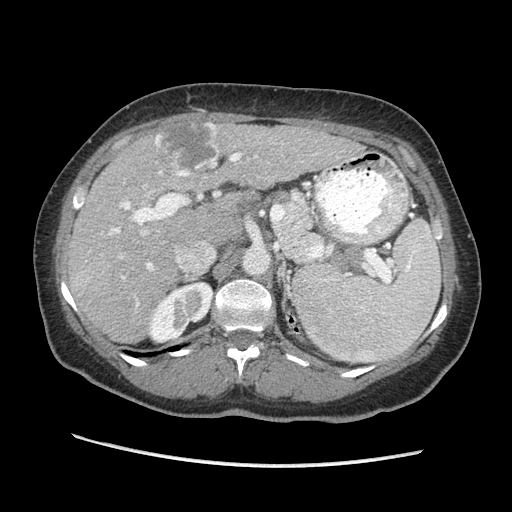
Contrast-enhanced abdominal CT (liver protocol), one axial slice. Slice 132 of 170 in the series (ordered by position). Reconstruction kernel STANDARD. 140 kVp. Soft-tissue window (W 400 / L 40 HU). 512 × 512 image matrix, field of view 360 × 360 mm. From the clinical record (not read from this slice): diagnosis: hepatocellular carcinoma (patient treated with transarterial chemoembolisation; whether this scan precedes or follows treatment is not stated here); TNM stage (as recorded): Stage-II; Child-Pugh class: A.
Outlined on this slice (semi-automatically segmented with operator editing):
- liver parenchyma outside the tumour (the mass and vessels are separate outlines, so this box may not span the whole liver): bounding box [x1, y1, x2, y2] px = [66, 122, 364, 342]
- mass: [154, 120, 217, 171]
- liver vessels: [109, 123, 355, 307]